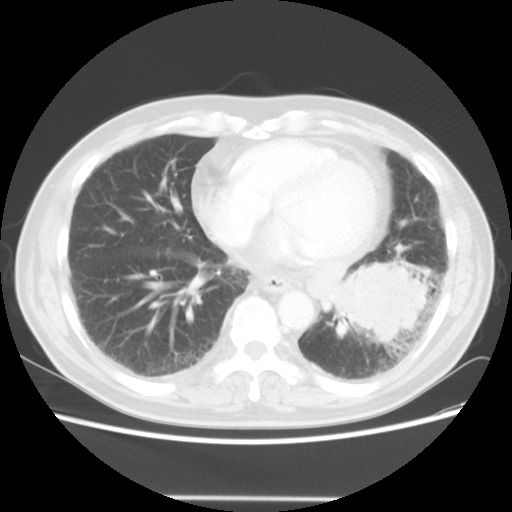
Chest CT, one axial slice. Position 17 of 56 along the scan axis. Lung window (W 1500 / L -600 HU). 512 × 512 image matrix, field of view 360 × 360 mm. Patient: male, 66 years. Case-level facts recorded for this patient, not image findings: clinical TNM (as recorded): T4 N3 M0; histopathological grade: G3.
Structures marked on this image (bounding box drawn by a radiologist):
- lung tumour (recorded histology: small cell carcinoma): box from (x=327, y=259) to (x=437, y=350) px